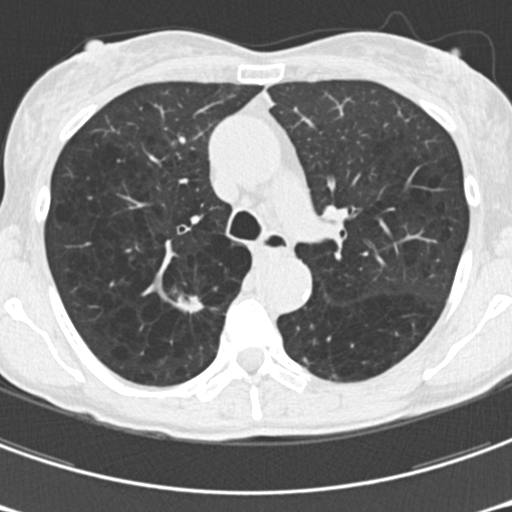
Low-dose screening chest CT, one axial slice. Slice 117 of 176 in the series (ordered by position). Reconstruction kernel B30f. 120 kVp. Lung window (W 1500 / L -600 HU). 2 mm slice thickness. 512 × 512 image matrix, field of view 277 × 277 mm.
Annotated regions visible in this slice (expert manual segmentation):
- lesion 1 (tumor, upper lobe of right lung): bounding box [x1, y1, x2, y2] px = [177, 296, 203, 313]